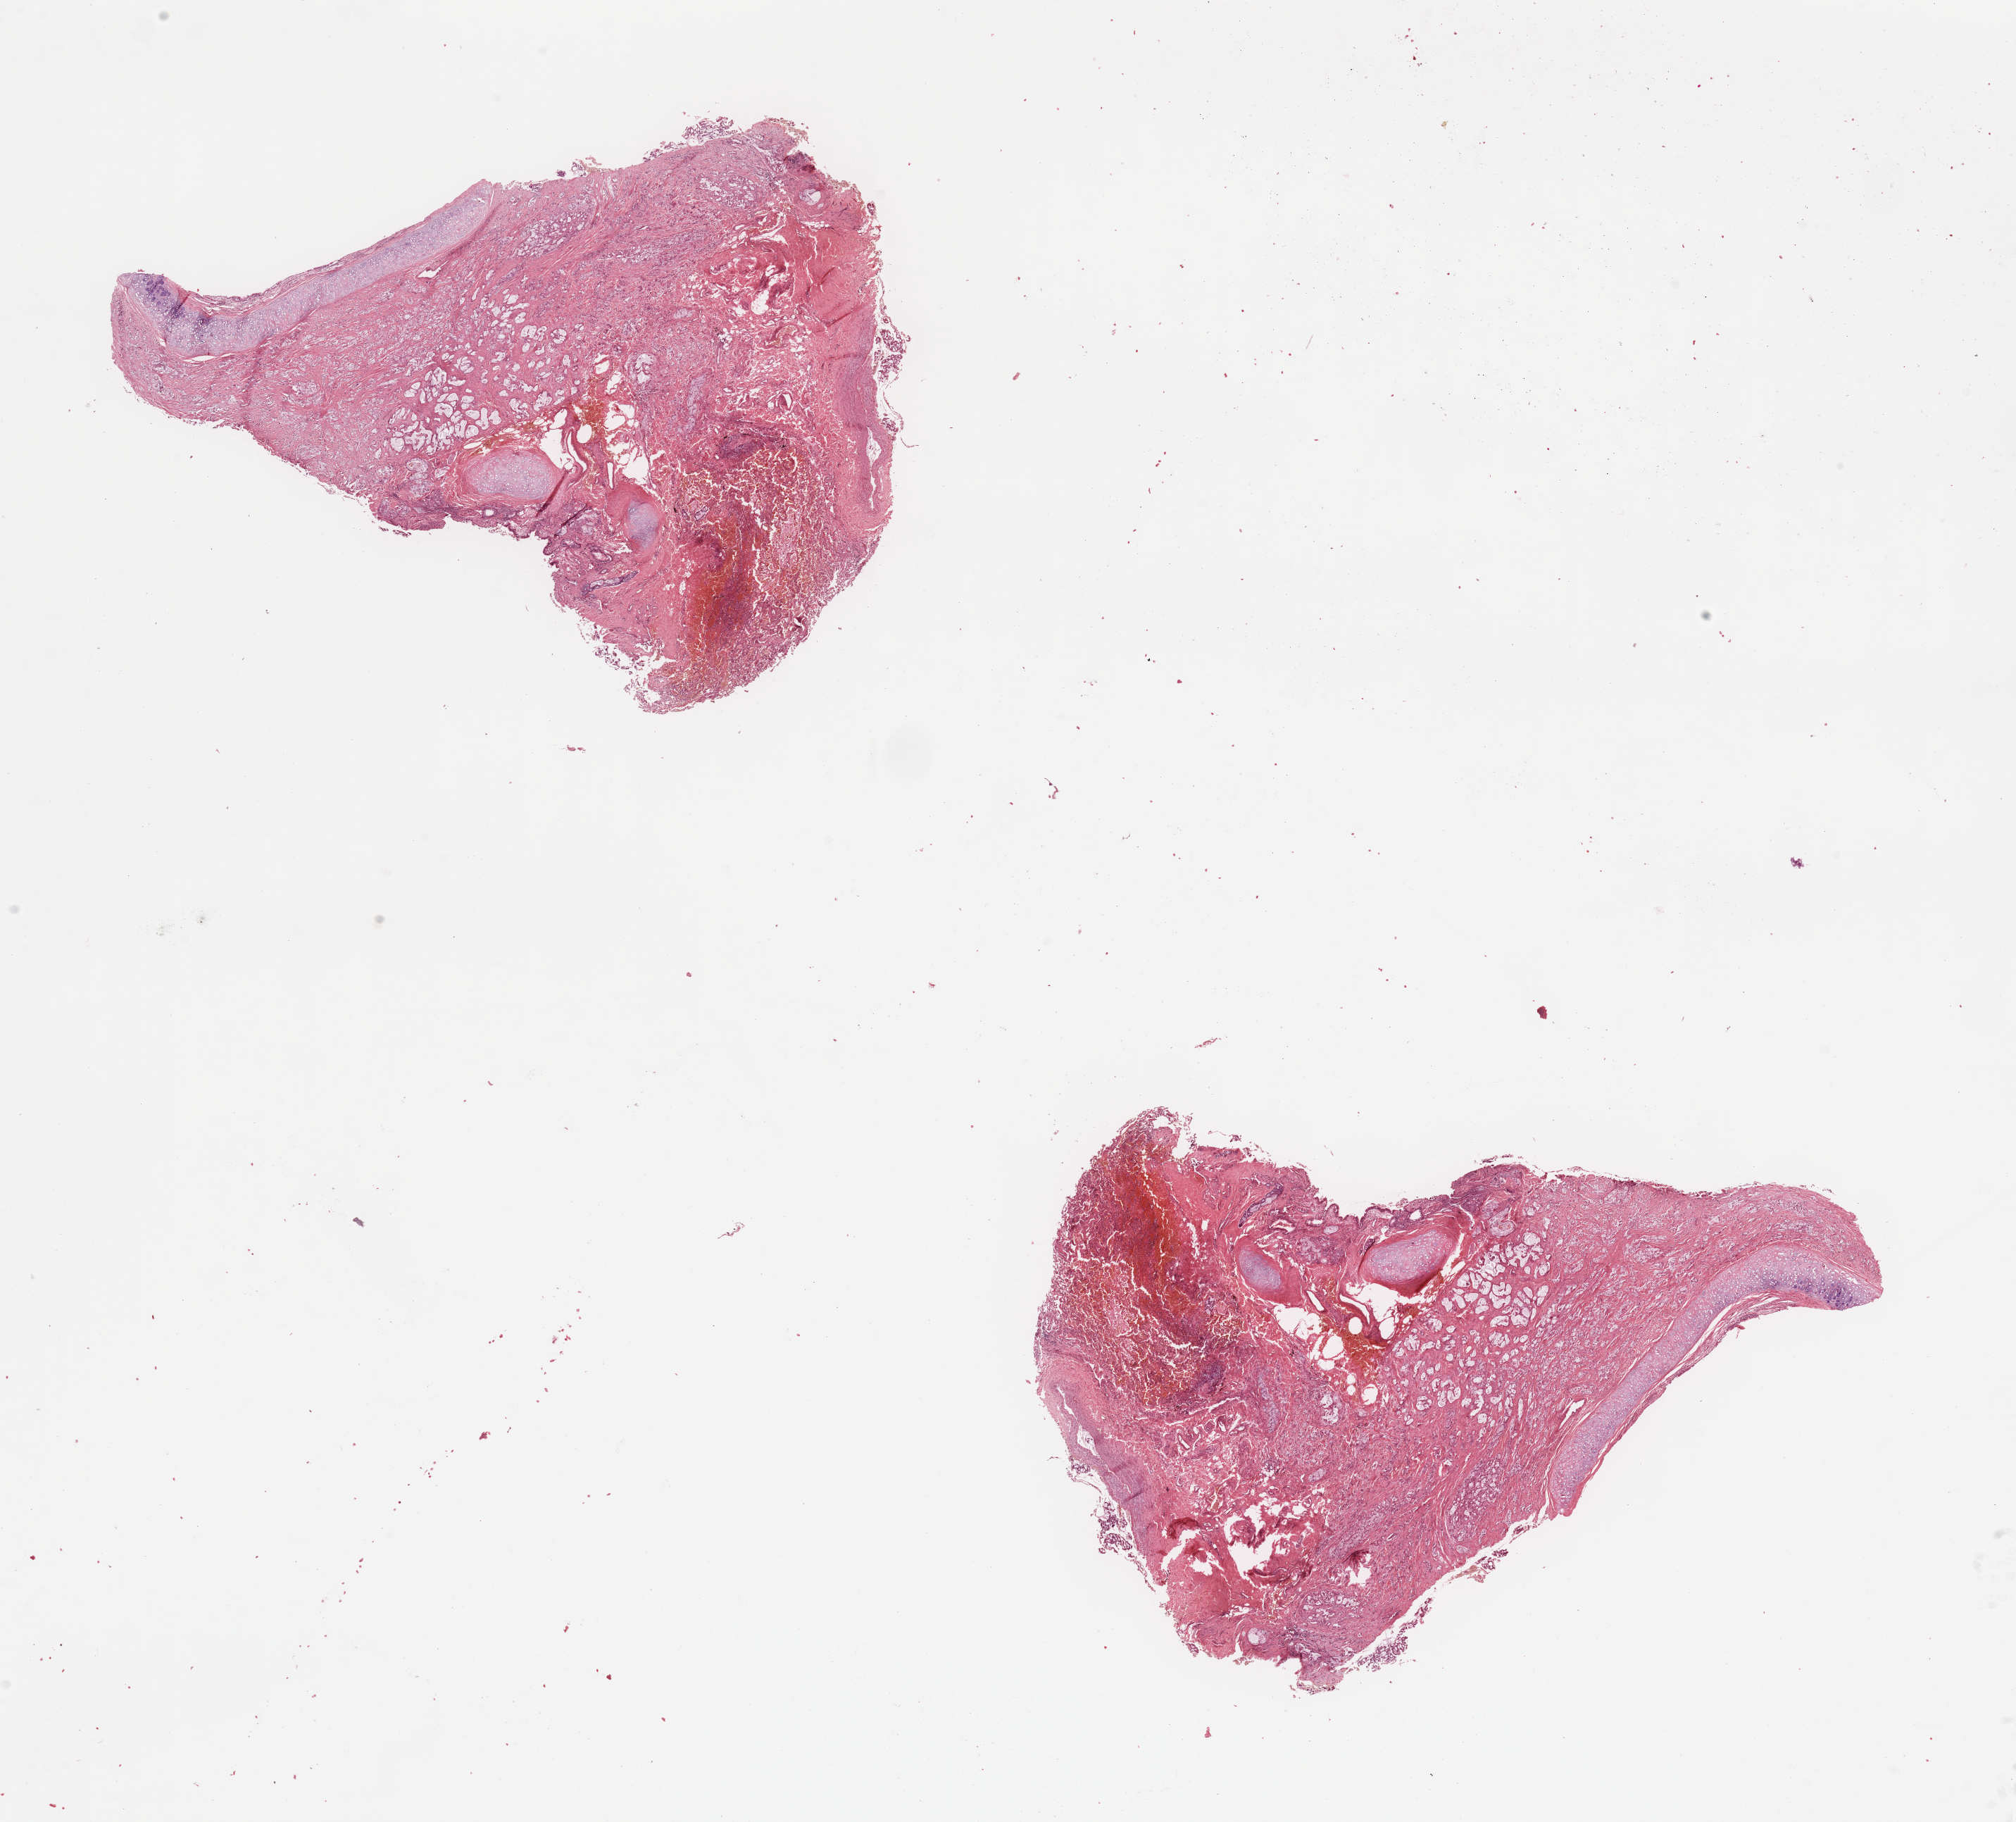
Digitized H&E tissue section (whole slide) — shown as a low-resolution overview of the whole scanned area (about 22.6 x 20.5 mm, slide scanned at 20x). Tumour tissue sample, lung. Female, 36 y/o.
Diagnosis: Adenocarcinoma, NOS.